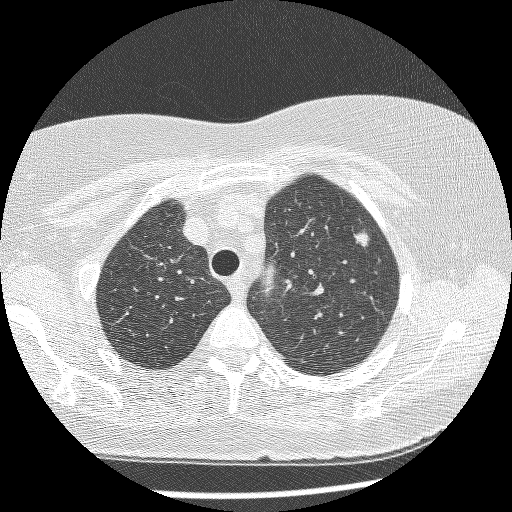
Chest CT (low-dose screening protocol), one axial image, baseline screening round, lung window (W 1500 / L -600 HU), 1.25 mm slice thickness, slice 186 of 241 in the series. Female, age 61 years at enrolment. Current smoker at enrolment.
• Lesion marked by an expert reader, bounding box (x1, y1, x2, y2) in pixels: (330, 221, 385, 270).
• The screening reader recorded 4 non-calcified nodules or masses ≥4 mm on this exam (right lower lobe, right middle lobe, right lower lobe, left upper lobe); which of them this box marks is not recorded.
• Official screen result: positive, change unspecified: nodule(s) >= 4 mm or enlarging nodule(s), mass(es), or other non-specific abnormalities suspicious for lung cancer.
• Participant outcome: lung cancer diagnosed 111 days after this screen — bronchiolo-alveolar adenocarcinoma, NOS, left upper lobe, stage IV (AJCC 6th edition), 10 mm at pathology.